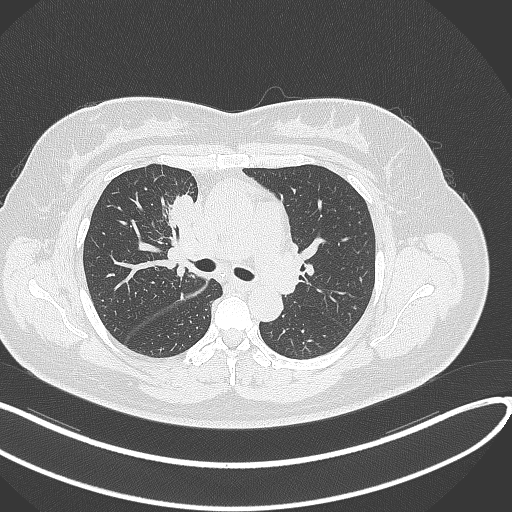
Chest CT, one axial slice. Slice 173 of 303 in the series (ordered by position). Reconstruction kernel B70f. Lung window (W 1500 / L -600 HU). 512 × 512 image matrix. Female patient, age 46 years. From the clinical record (not read from this slice): clinical TNM (as recorded): T2a N1 M0.
Annotated regions visible in this slice (bounding box drawn by a radiologist):
- lung tumour (recorded histology: adenocarcinoma): bounding box (x1, y1, x2, y2) in pixels: (168, 191, 200, 234)